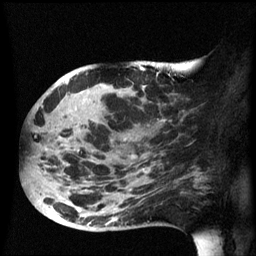
Breast MRI (dynamic contrast-enhanced), one sagittal slice; position 27 of 60 along the scan axis; dynamic contrast-enhanced series, image 2 of 3 at this slice position (ordered by acquisition); 1.5 T; TE 4.2 ms, TR 8.4 ms; 256 × 256 image matrix. Female patient, age 49 years.
Structures marked on this image (semi-automatic segmentation, software-assisted and operator-edited):
- analysis volume of interest (the breast-tissue region the enhancement analysis was run in; not a lesion): bounding box (x1, y1, x2, y2) in pixels: (24, 72, 185, 233)
- tumour enhancement mask (voxels above the 70 % enhancement threshold inside the analysis volume of interest): (49, 80, 166, 225)